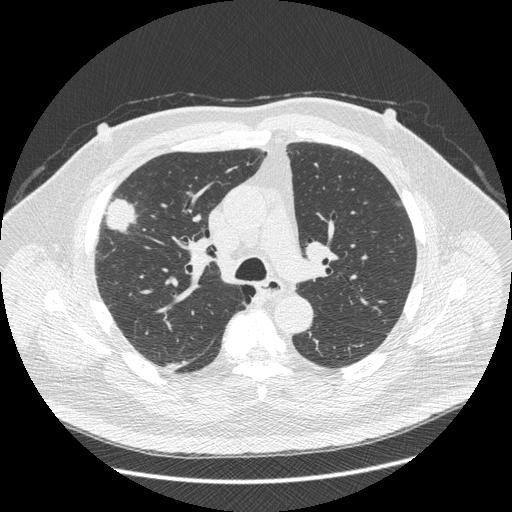
Chest CT (low-dose screening protocol), one axial image. Third annual screen. Lung window (W 1500 / L -600 HU). Standard (soft-tissue) reconstruction kernel (STANDARD). 120 kVp. 512 × 512 image matrix, field of view 400 × 400 mm. Male participant, aged 66 years at enrolment.
• Expert-annotated lung lesion, bounding box <86,183,145,265> (left, top, right, bottom; pixels).
• The exam's reader record, not a measurement of the box and not confirmed to be the same lesion: non-calcified nodule or mass ≥4 mm, right upper lobe, 48 × 25 mm, spiculated (stellate) margins, soft tissue attenuation, pre-existing on the prior screen: no.